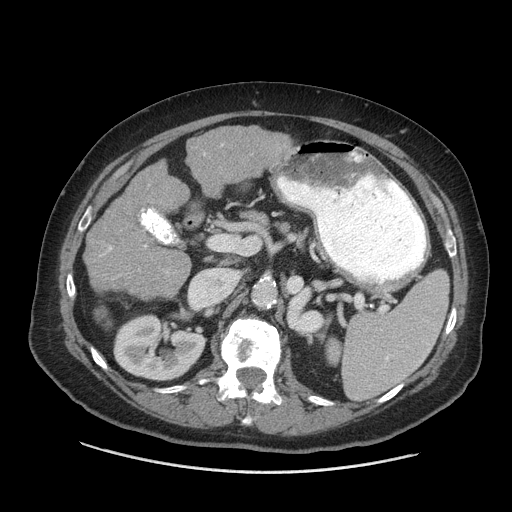
Contrast-enhanced abdominal CT (liver protocol), one axial slice; reconstruction kernel STANDARD; soft-tissue window (W 400 / L 40 HU); 512 × 512 image matrix, field of view 420 × 420 mm. From the clinical record (not read from this slice): diagnosis: hepatocellular carcinoma (patient treated with transarterial chemoembolisation; whether this scan precedes or follows treatment is not stated here); TNM stage (as recorded): Stage-I; Child-Pugh class: A; tumour differentiation: well differentiated.
Annotated regions visible in this slice (semi-automatic segmentation, software-assisted and operator-edited):
- liver parenchyma outside the tumour (the mass and vessels are separate outlines, so this box may not span the whole liver): box from (x=84, y=126) to (x=294, y=286) px
- liver vessels: (x=109, y=245)–(x=146, y=251)